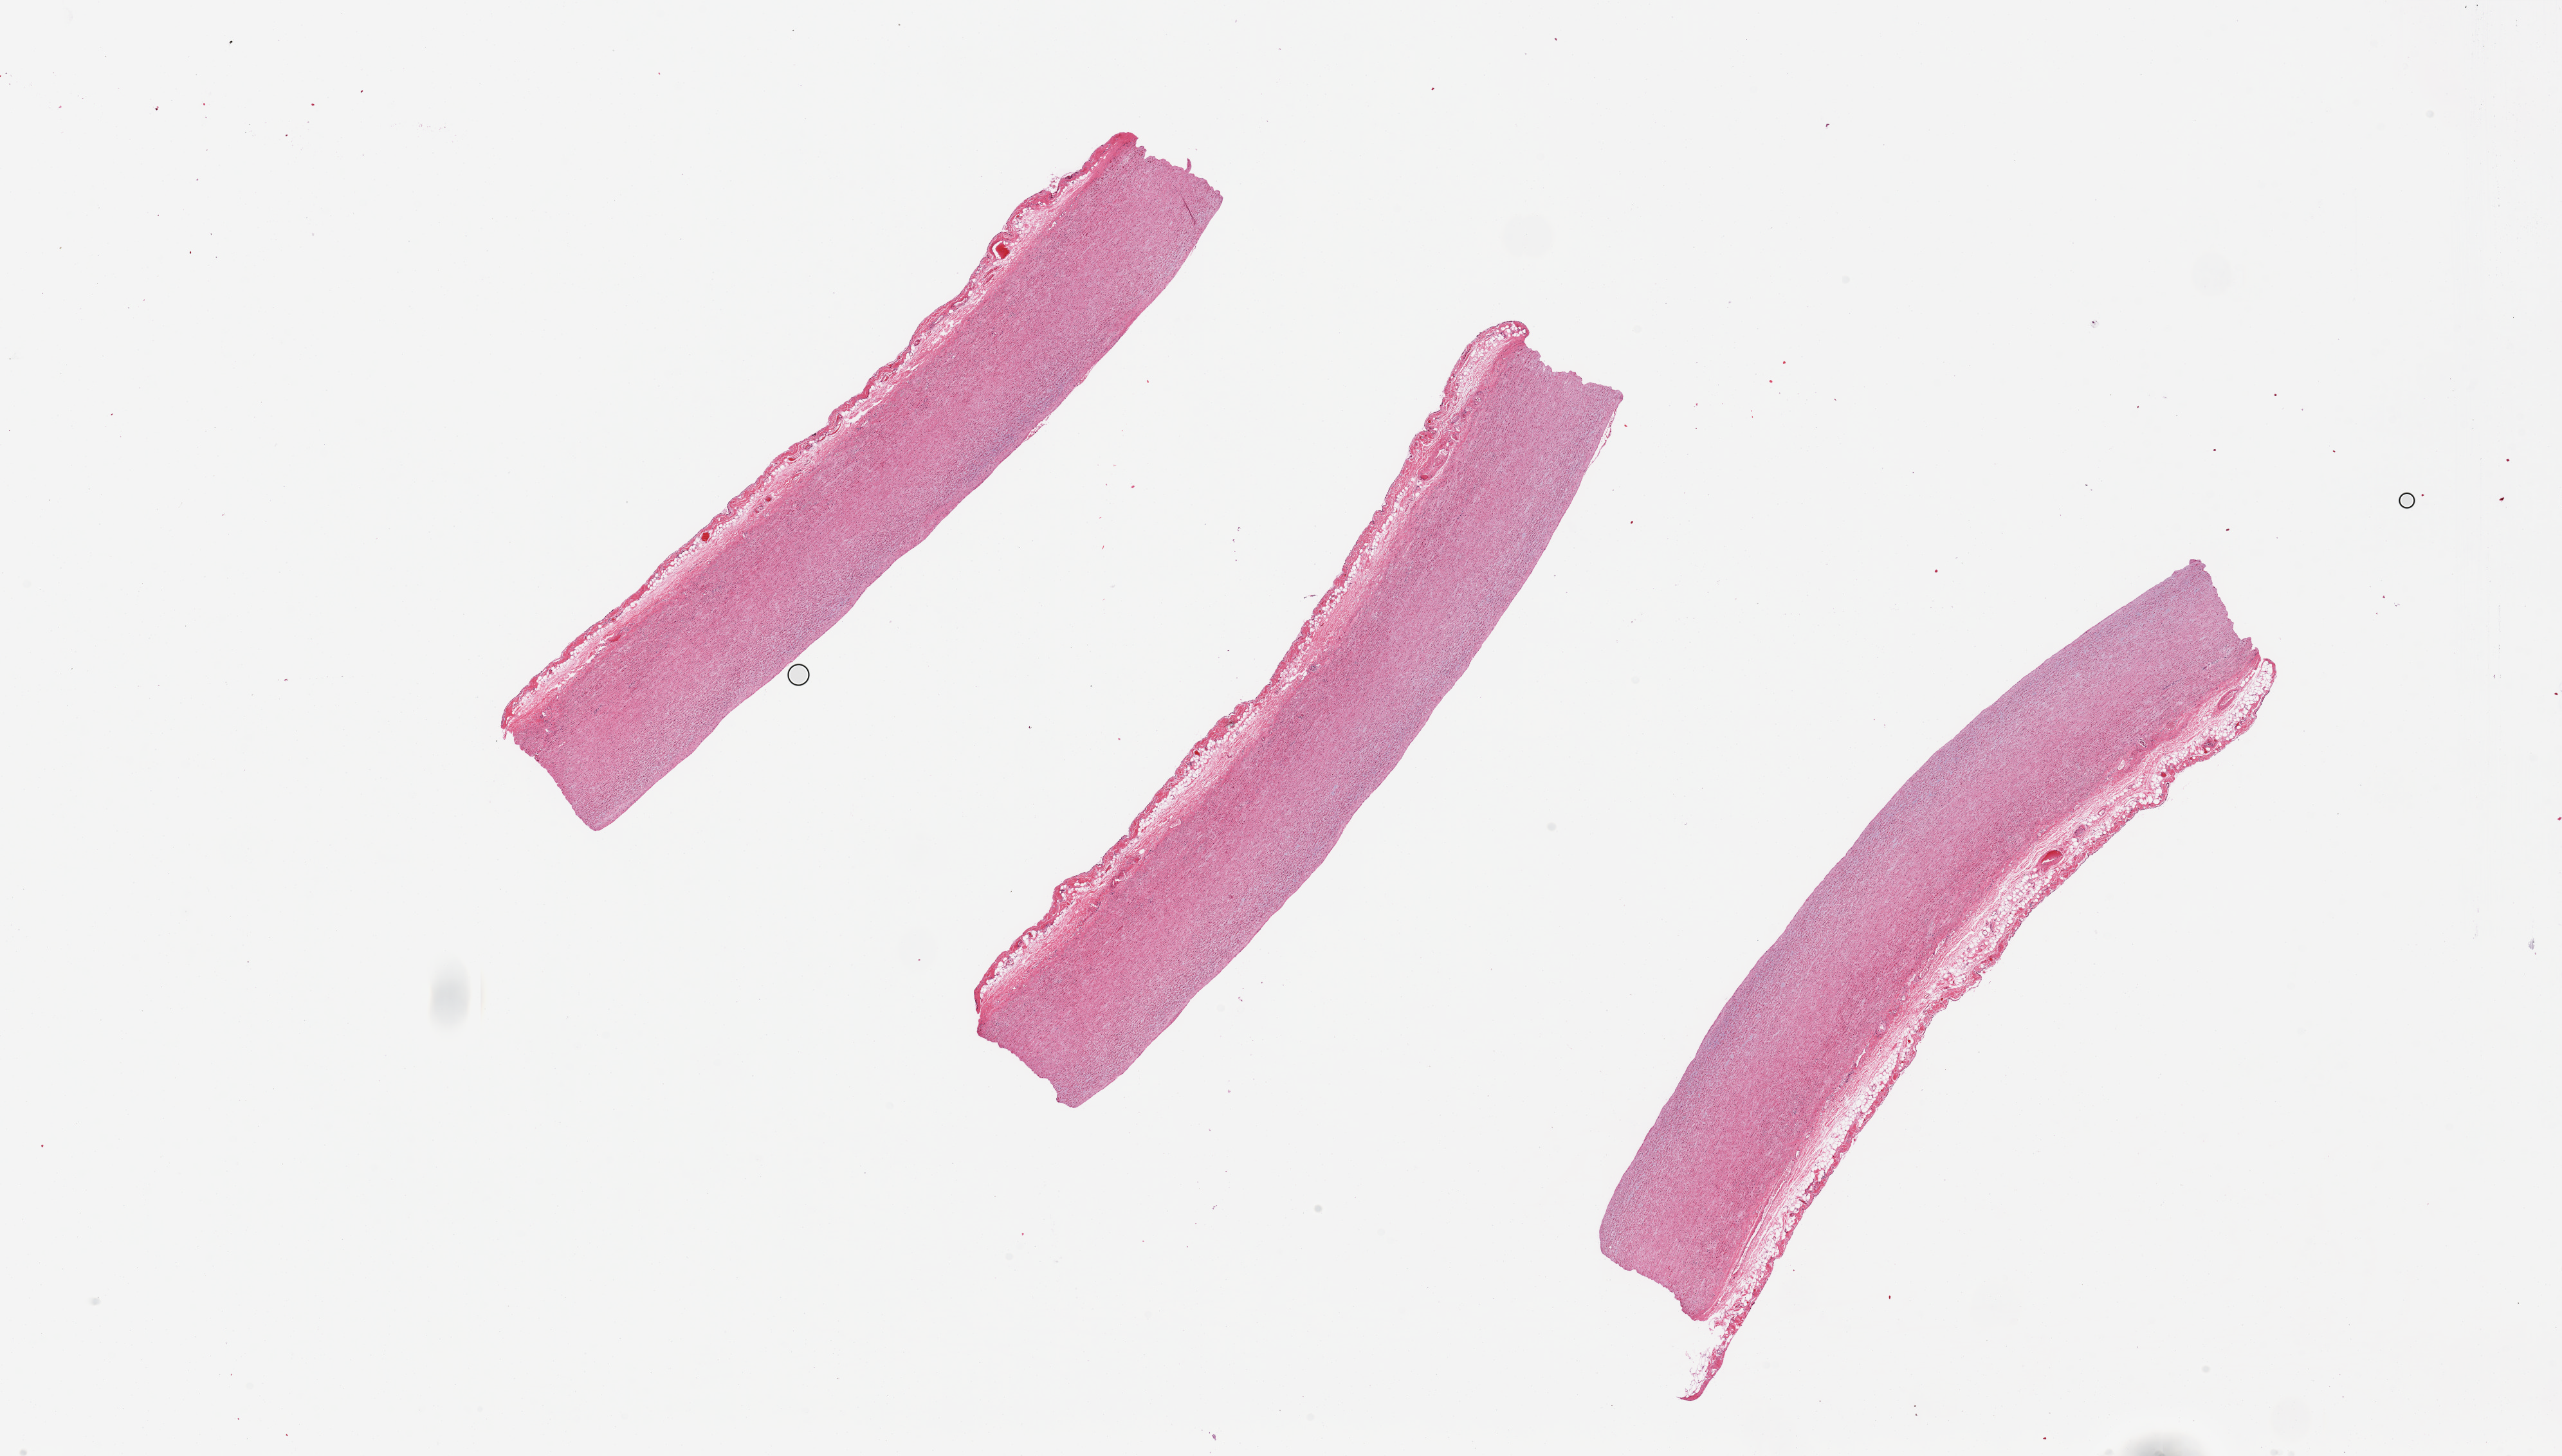
Digitized hematoxylin and eosin (H&E)-stained section, brightfield — a low-resolution overview of the entire scanned area, about 31.5 x 17.9 mm (from a 20x scan), PAXgene-fixed paraffin-embedded (PFPE) section, section of aorta (target tissue), tissue donor sample. Male donor.
Pathologist's review note for this sample: Minimal atherosis.